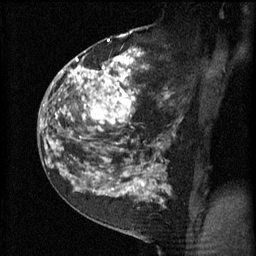
Breast MRI (dynamic contrast-enhanced), one sagittal slice; position 31 of 60 along the scan axis; 3 images stored at this slice position (order not interpretable as contrast timing); 1.5 T; TE 4.2 ms, TR 11 ms; 2 mm slice thickness; 256 × 256 image matrix, field of view 180 × 180 mm. Patient: female, 52 years.
Structures marked on this image (semi-automatically segmented with operator editing):
- analysis volume of interest (the breast-tissue region the enhancement analysis was run in; not a lesion): bounding box [x1, y1, x2, y2] px = [81, 52, 171, 157]
- tumour enhancement mask (voxels above the 70 % enhancement threshold inside the analysis volume of interest): [81, 52, 169, 151]